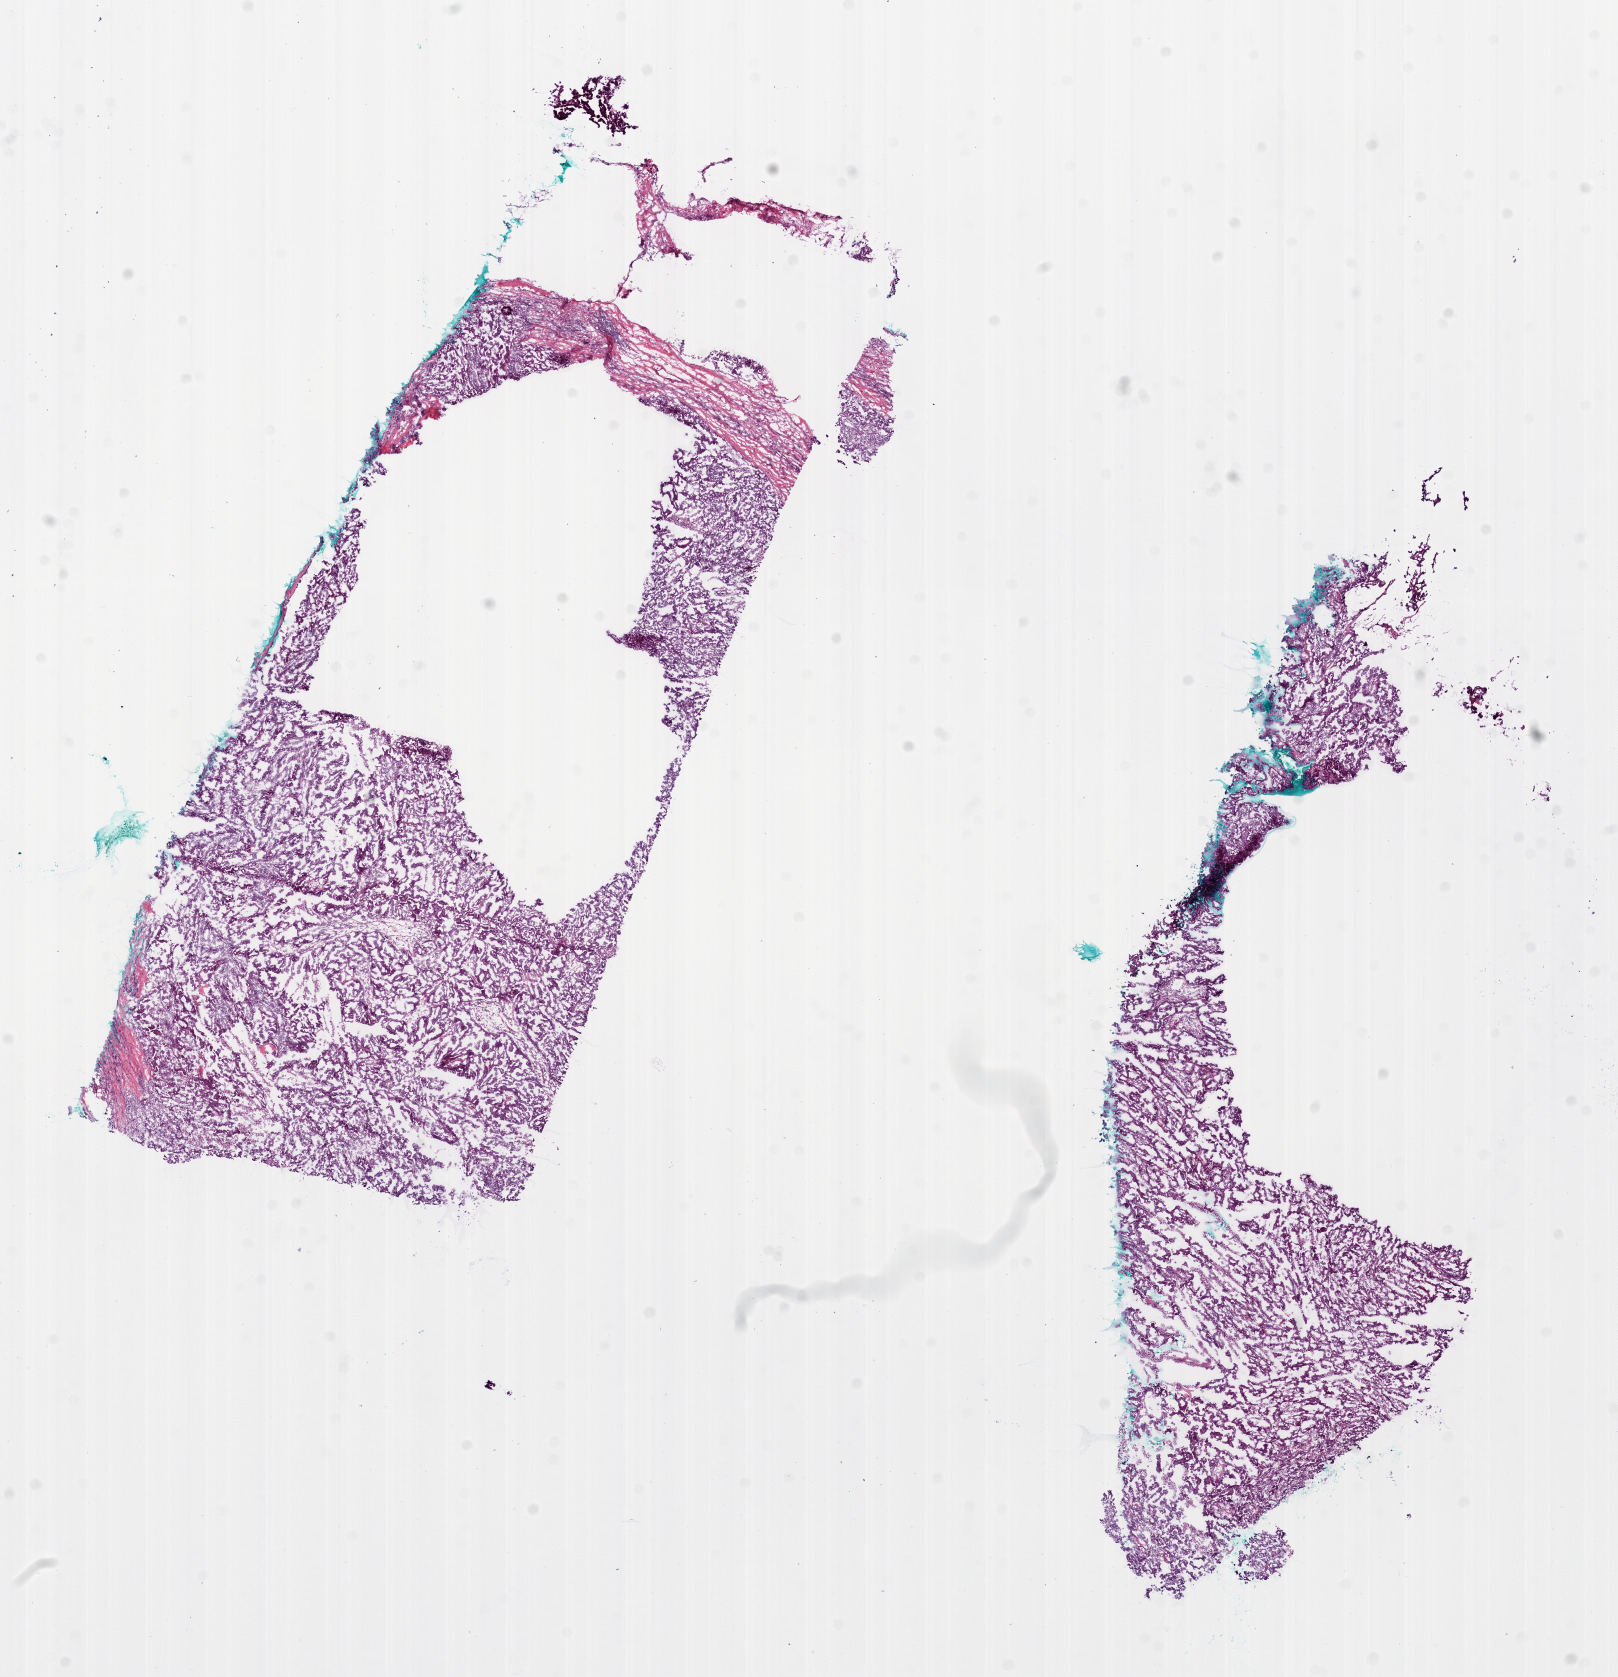
Digitized H&E-stained tissue section (whole slide) — shown as a low-resolution overview of the whole scanned area (about 13.1 x 13.5 mm, acquisition: 20x scan). Frozen section from the bottom of the tissue portion. Ovary, primary tumour sample. Patient: female, age at initial diagnosis 63 years. Histologic grade: G3 (poorly differentiated). Composition of this section per pathologist review: tumour cells 77%, tumour nuclei 80%, normal cells 18%, stromal cells 2%, necrosis 3%. Infiltration values recorded for this section: lymphocyte infiltration 70%, neutrophil infiltration 30%.
Laterality: bilateral. Diagnosis: Serous cystadenocarcinoma, NOS. FIGO stage: IIIC.